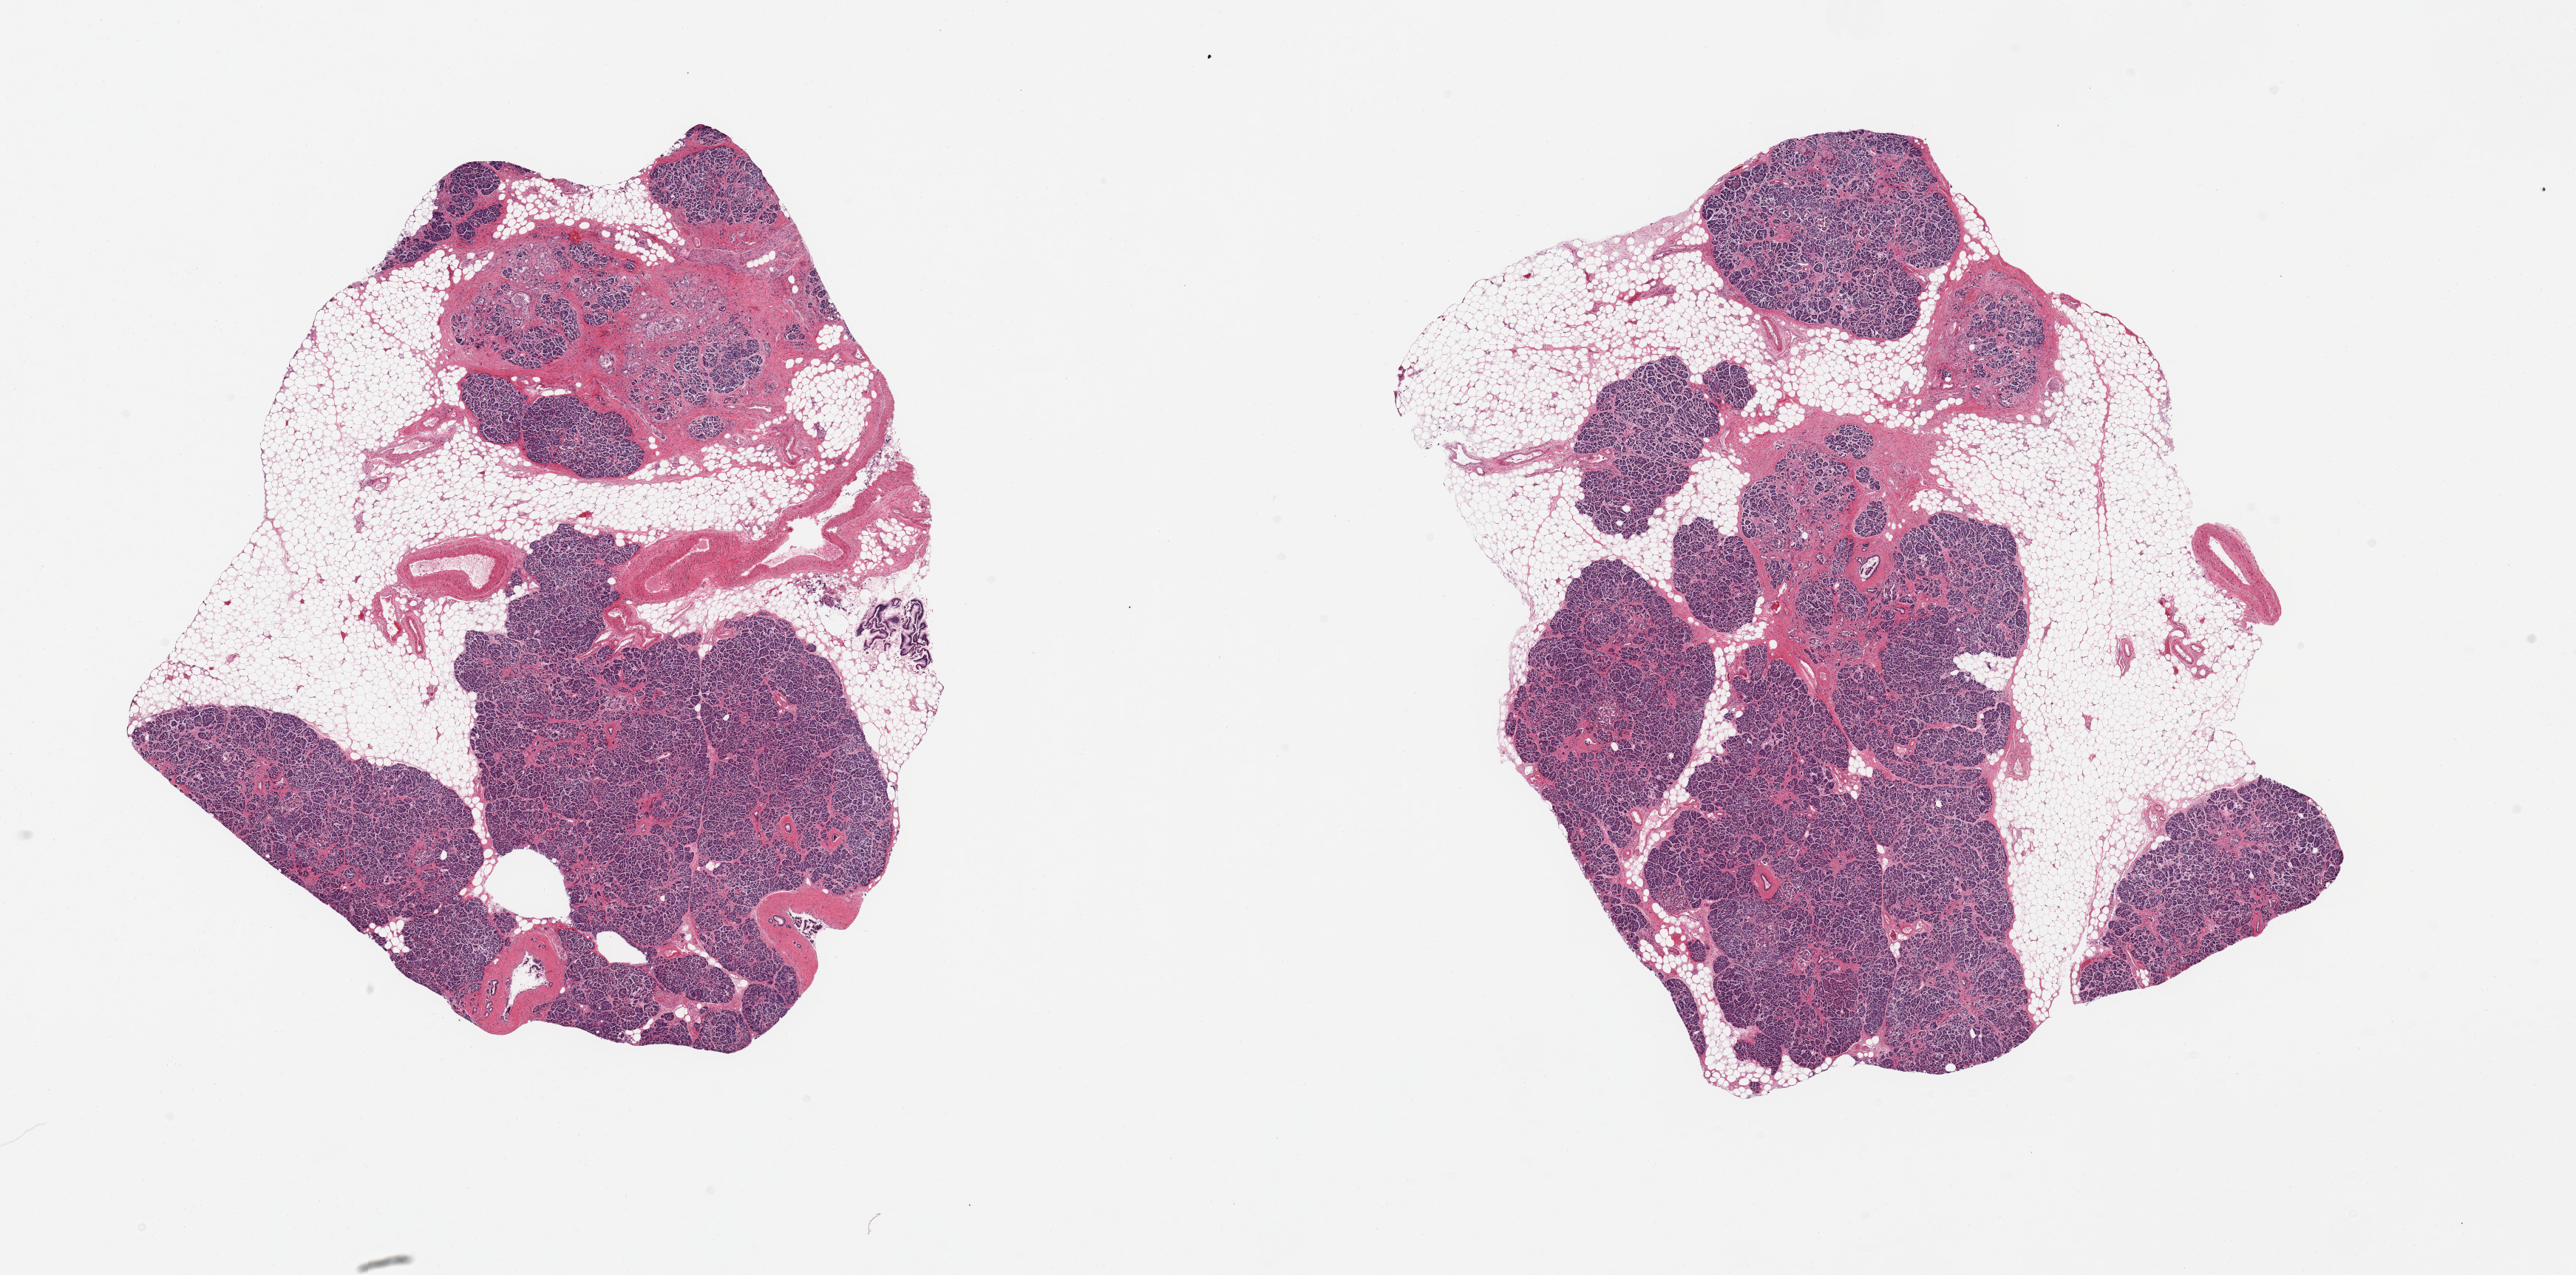
Digitized H&E-stained section, whole scanned area (about 27.6 x 13.6 mm, from a 20x scan) shown as a low-resolution overview, PAXgene-fixed paraffin-embedded (PFPE) section, sampled site (target tissue): pancreas, tissue donor sample. Donor: male.
Pathologist's review note for this sample: 2 pieces, moderate saponification; Patchy chronic pancreatitis, remoted; ~30% adherent /interstitial fat.